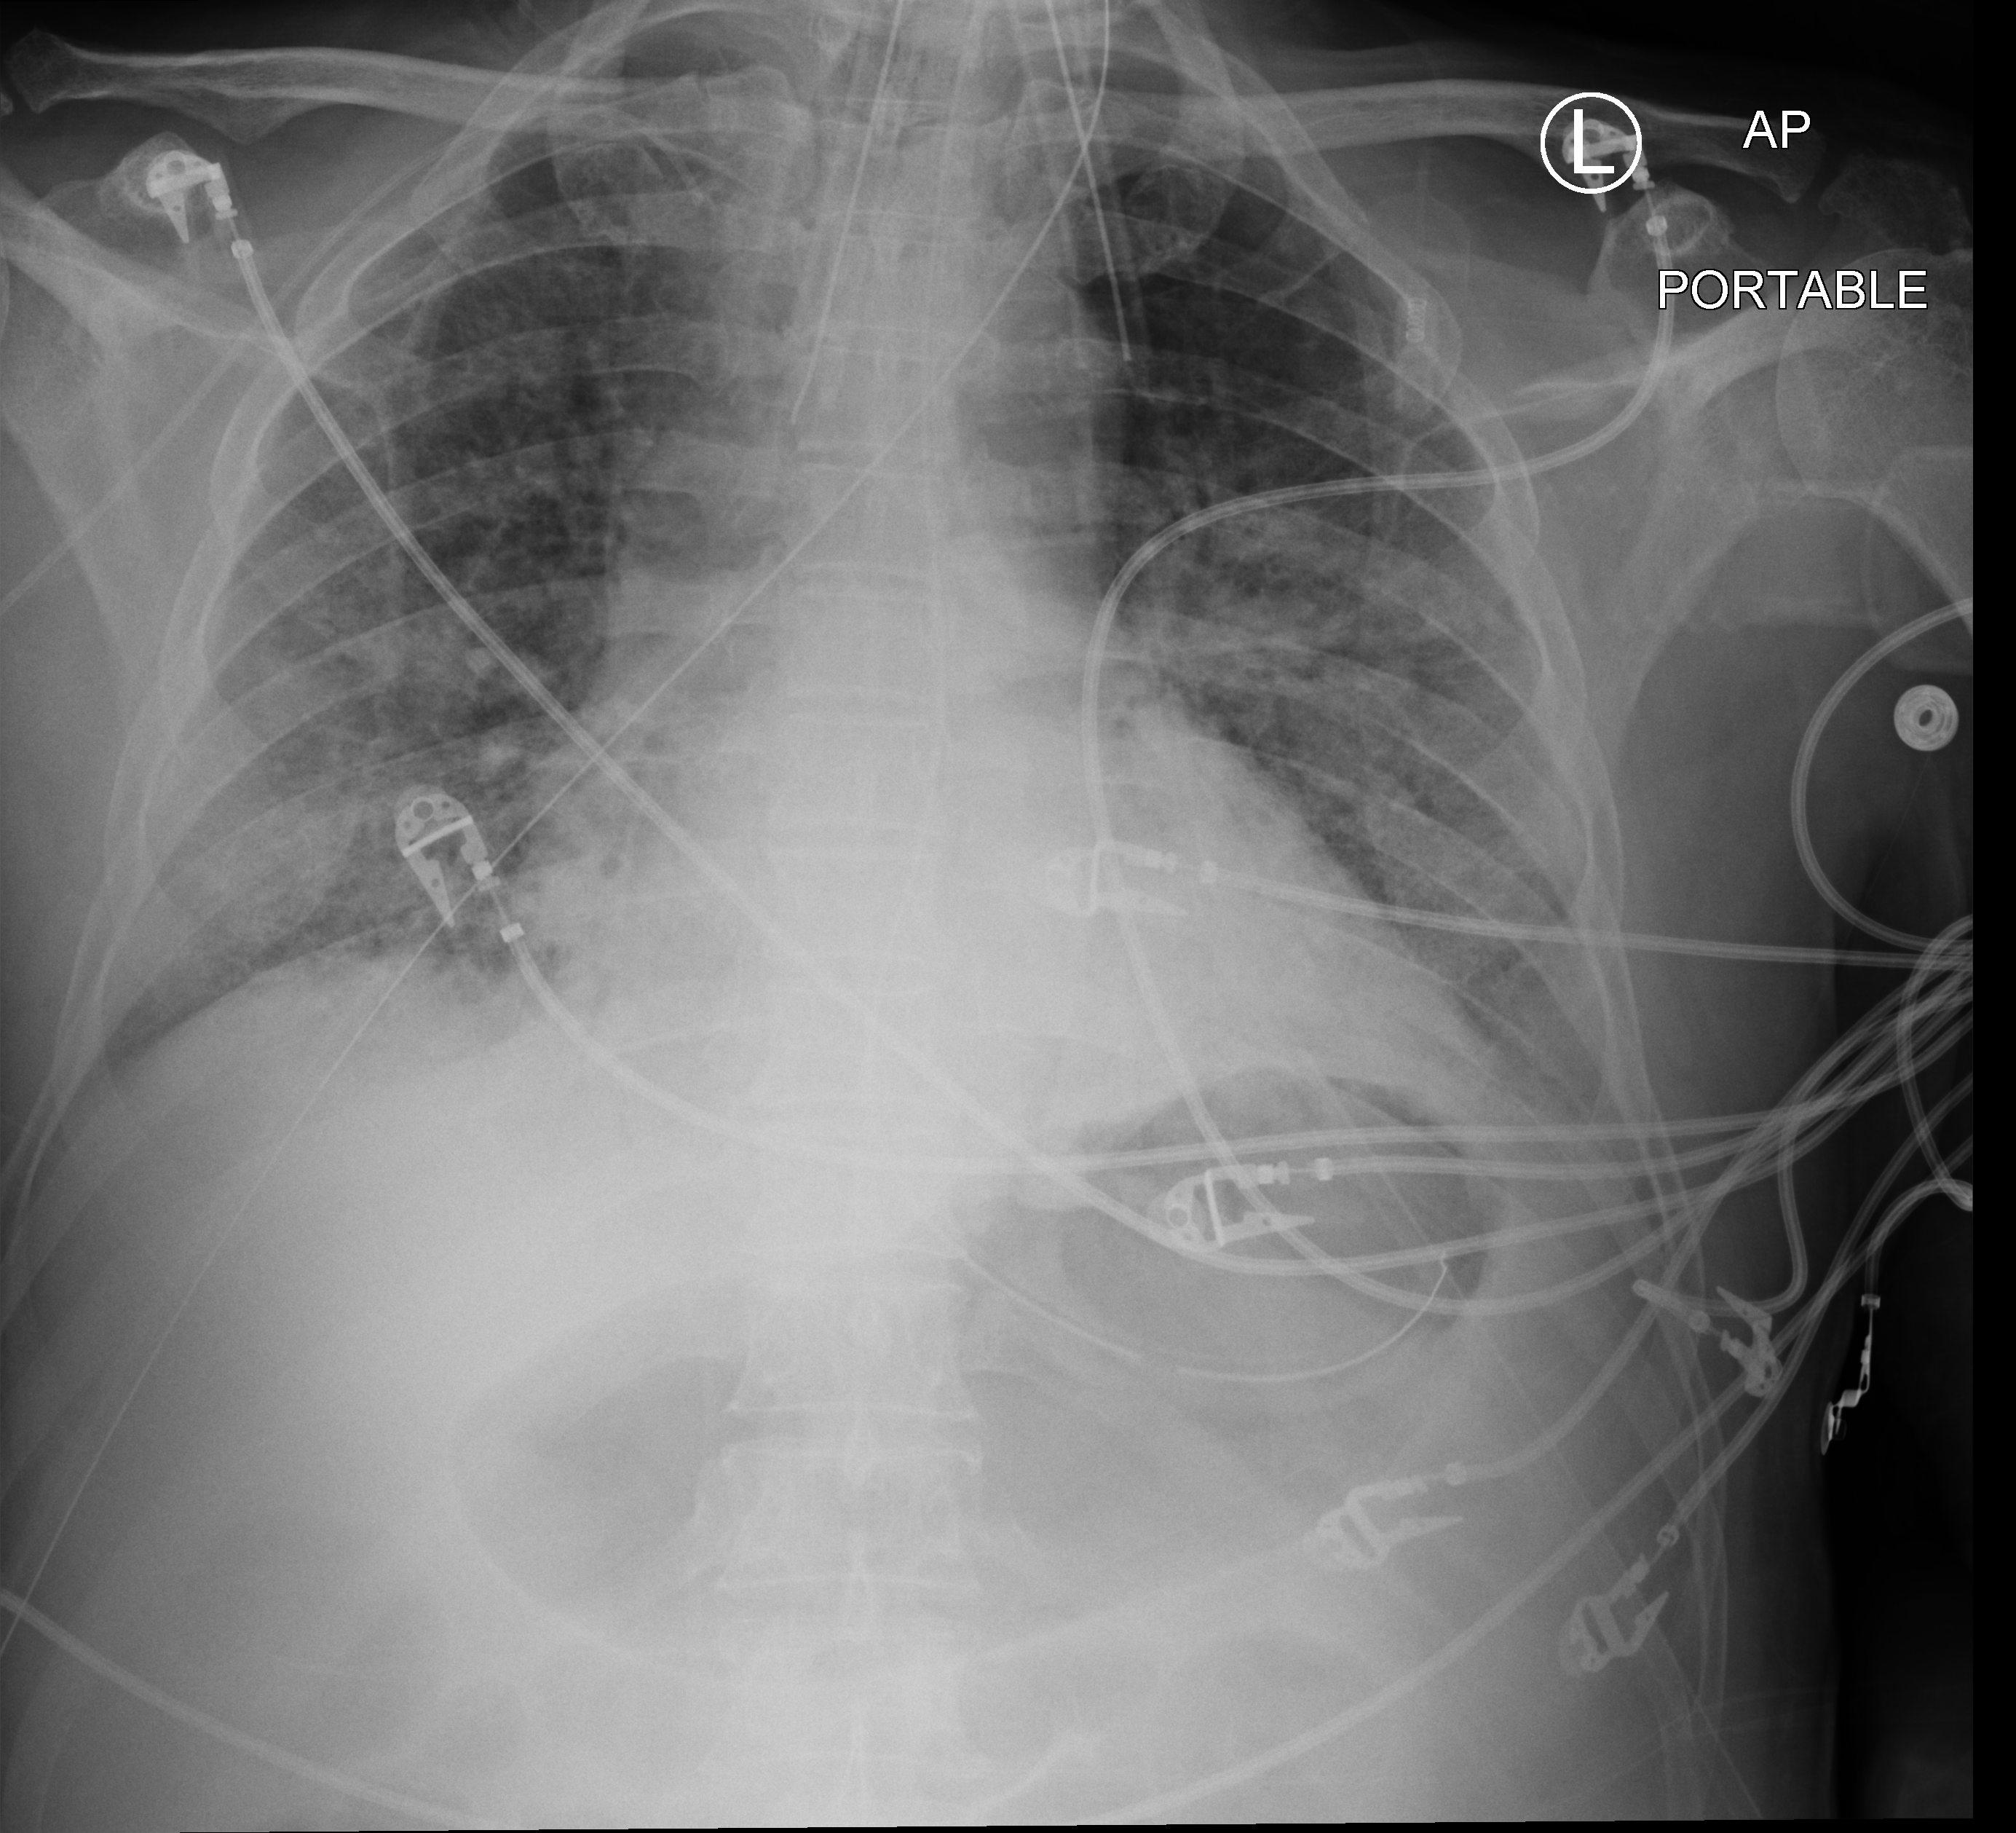
Chest X-ray (portable); anteroposterior (AP) projection. Male patient hospitalised with COVID-19, age 60–74 years.
Admission-level facts for this patient (not findings on this image; timing relative to this image not recorded):
- length of hospital stay: 37 days